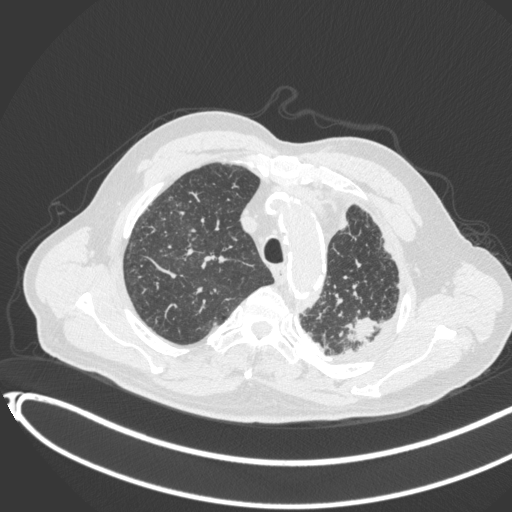
Chest CT, one axial slice; position 340 of 451 along the scan axis; reconstruction kernel B31f; 120 kVp; lung window (W 1500 / L -600 HU); 1 mm slice thickness; 512 × 512 image matrix. Male patient, age 78 years. Case-level facts recorded for this patient, not image findings: clinical TNM (as recorded): T1c N0 M1.
Structures marked on this image (rectangle marked by the reading radiologist):
- lung tumour (recorded histology: adenocarcinoma): bounding box <345,311,380,345> (left, top, right, bottom; pixels)